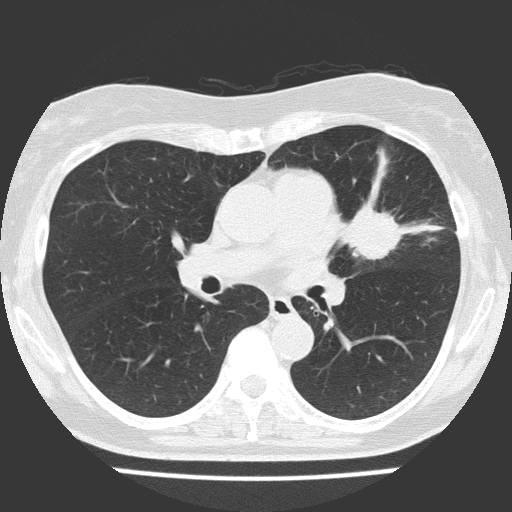
Chest CT (low-dose screening protocol), one axial image; first (baseline) screen; lung window (W 1500 / L -600 HU); 2 mm slice thickness; lung (sharp) reconstruction kernel (FC51); 120 kVp; slice 70 of 151 in the series. Female participant, aged 70 years at enrolment. Current smoker at enrolment.
- Lesion marked by an expert reader, bounding box <323,183,432,276> (left, top, right, bottom; pixels).
- The screening reader recorded 2 non-calcified nodules or masses ≥4 mm on this exam; which of them this box marks is not recorded.
- Lung cancer was diagnosed 25 days after this screen: adenocarcinoma, NOS, left upper lobe, poorly differentiated (G3), stage IV (AJCC 6th edition), 30 mm at pathology.